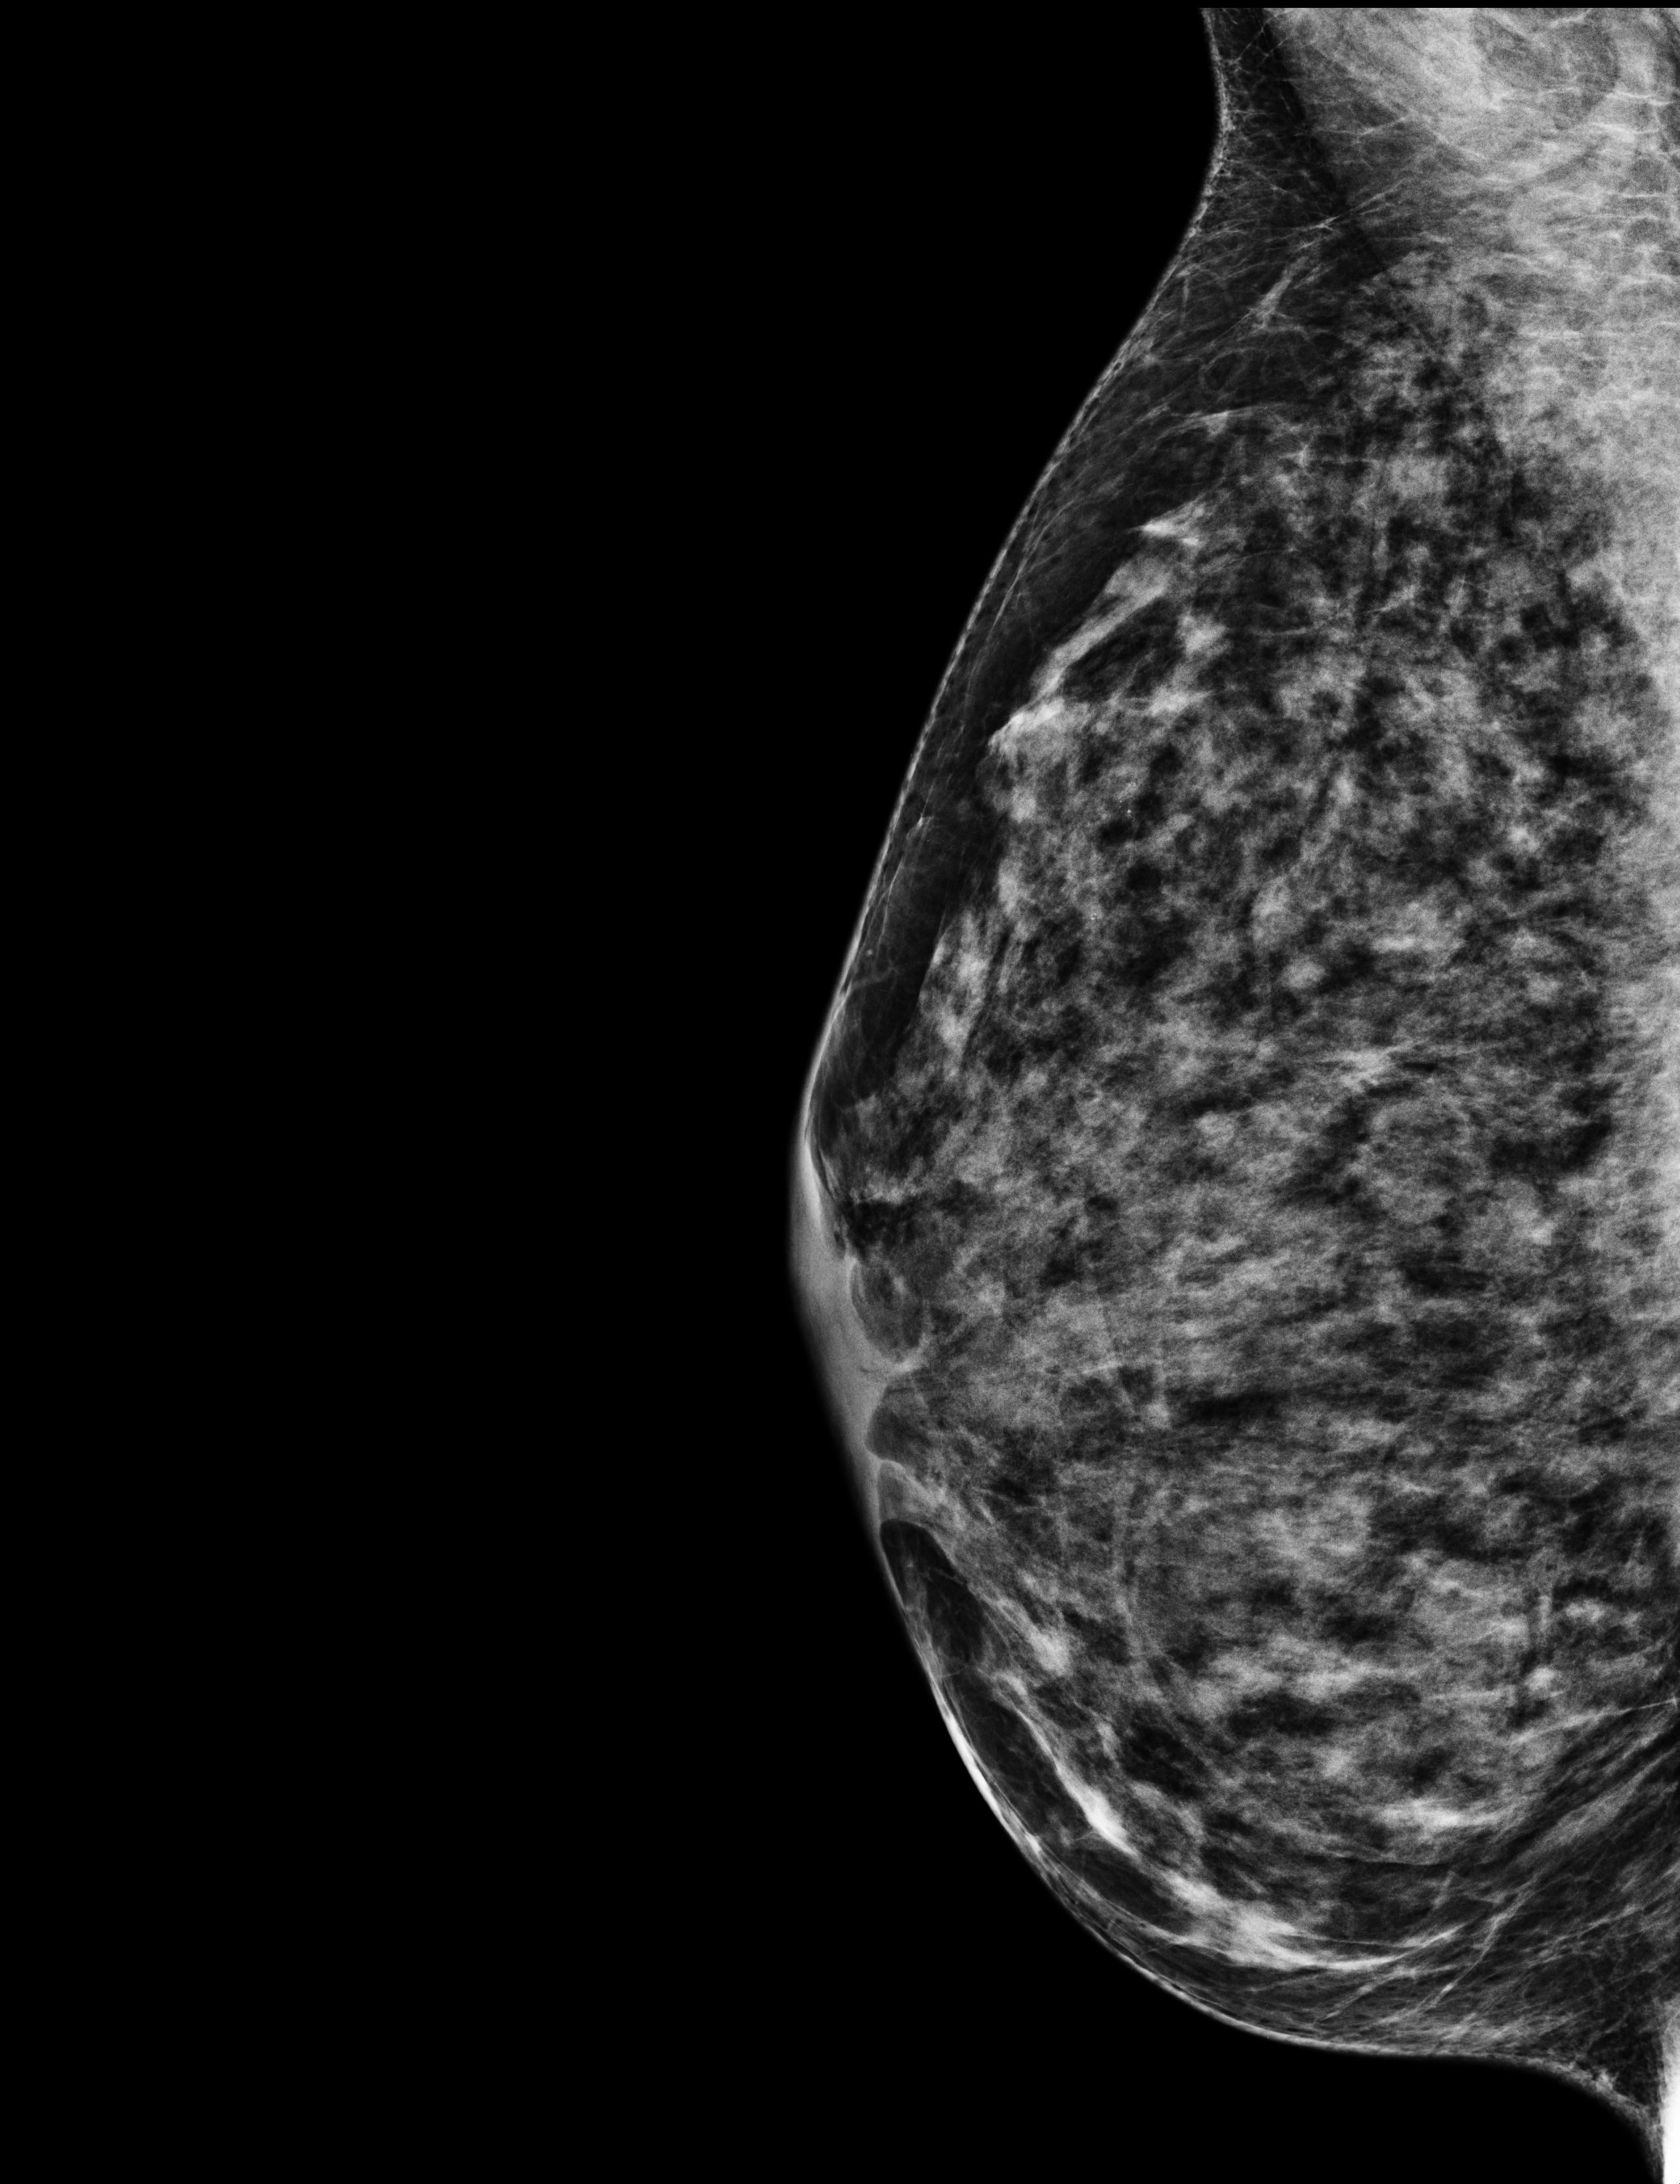
Screening examination; system: Selenia Dimensions. Patient aged 52 years (female).
Image type: full-field digital mammogram. Breast: right. Projection: mediolateral oblique (MLO) view. Breast density at the screening exam (both breasts): heterogeneously dense (BI-RADS density category c). Final BI-RADS category for the screening round (tomosynthesis exam, both breasts): category 2. Recall: recalled for additional imaging after this screen.